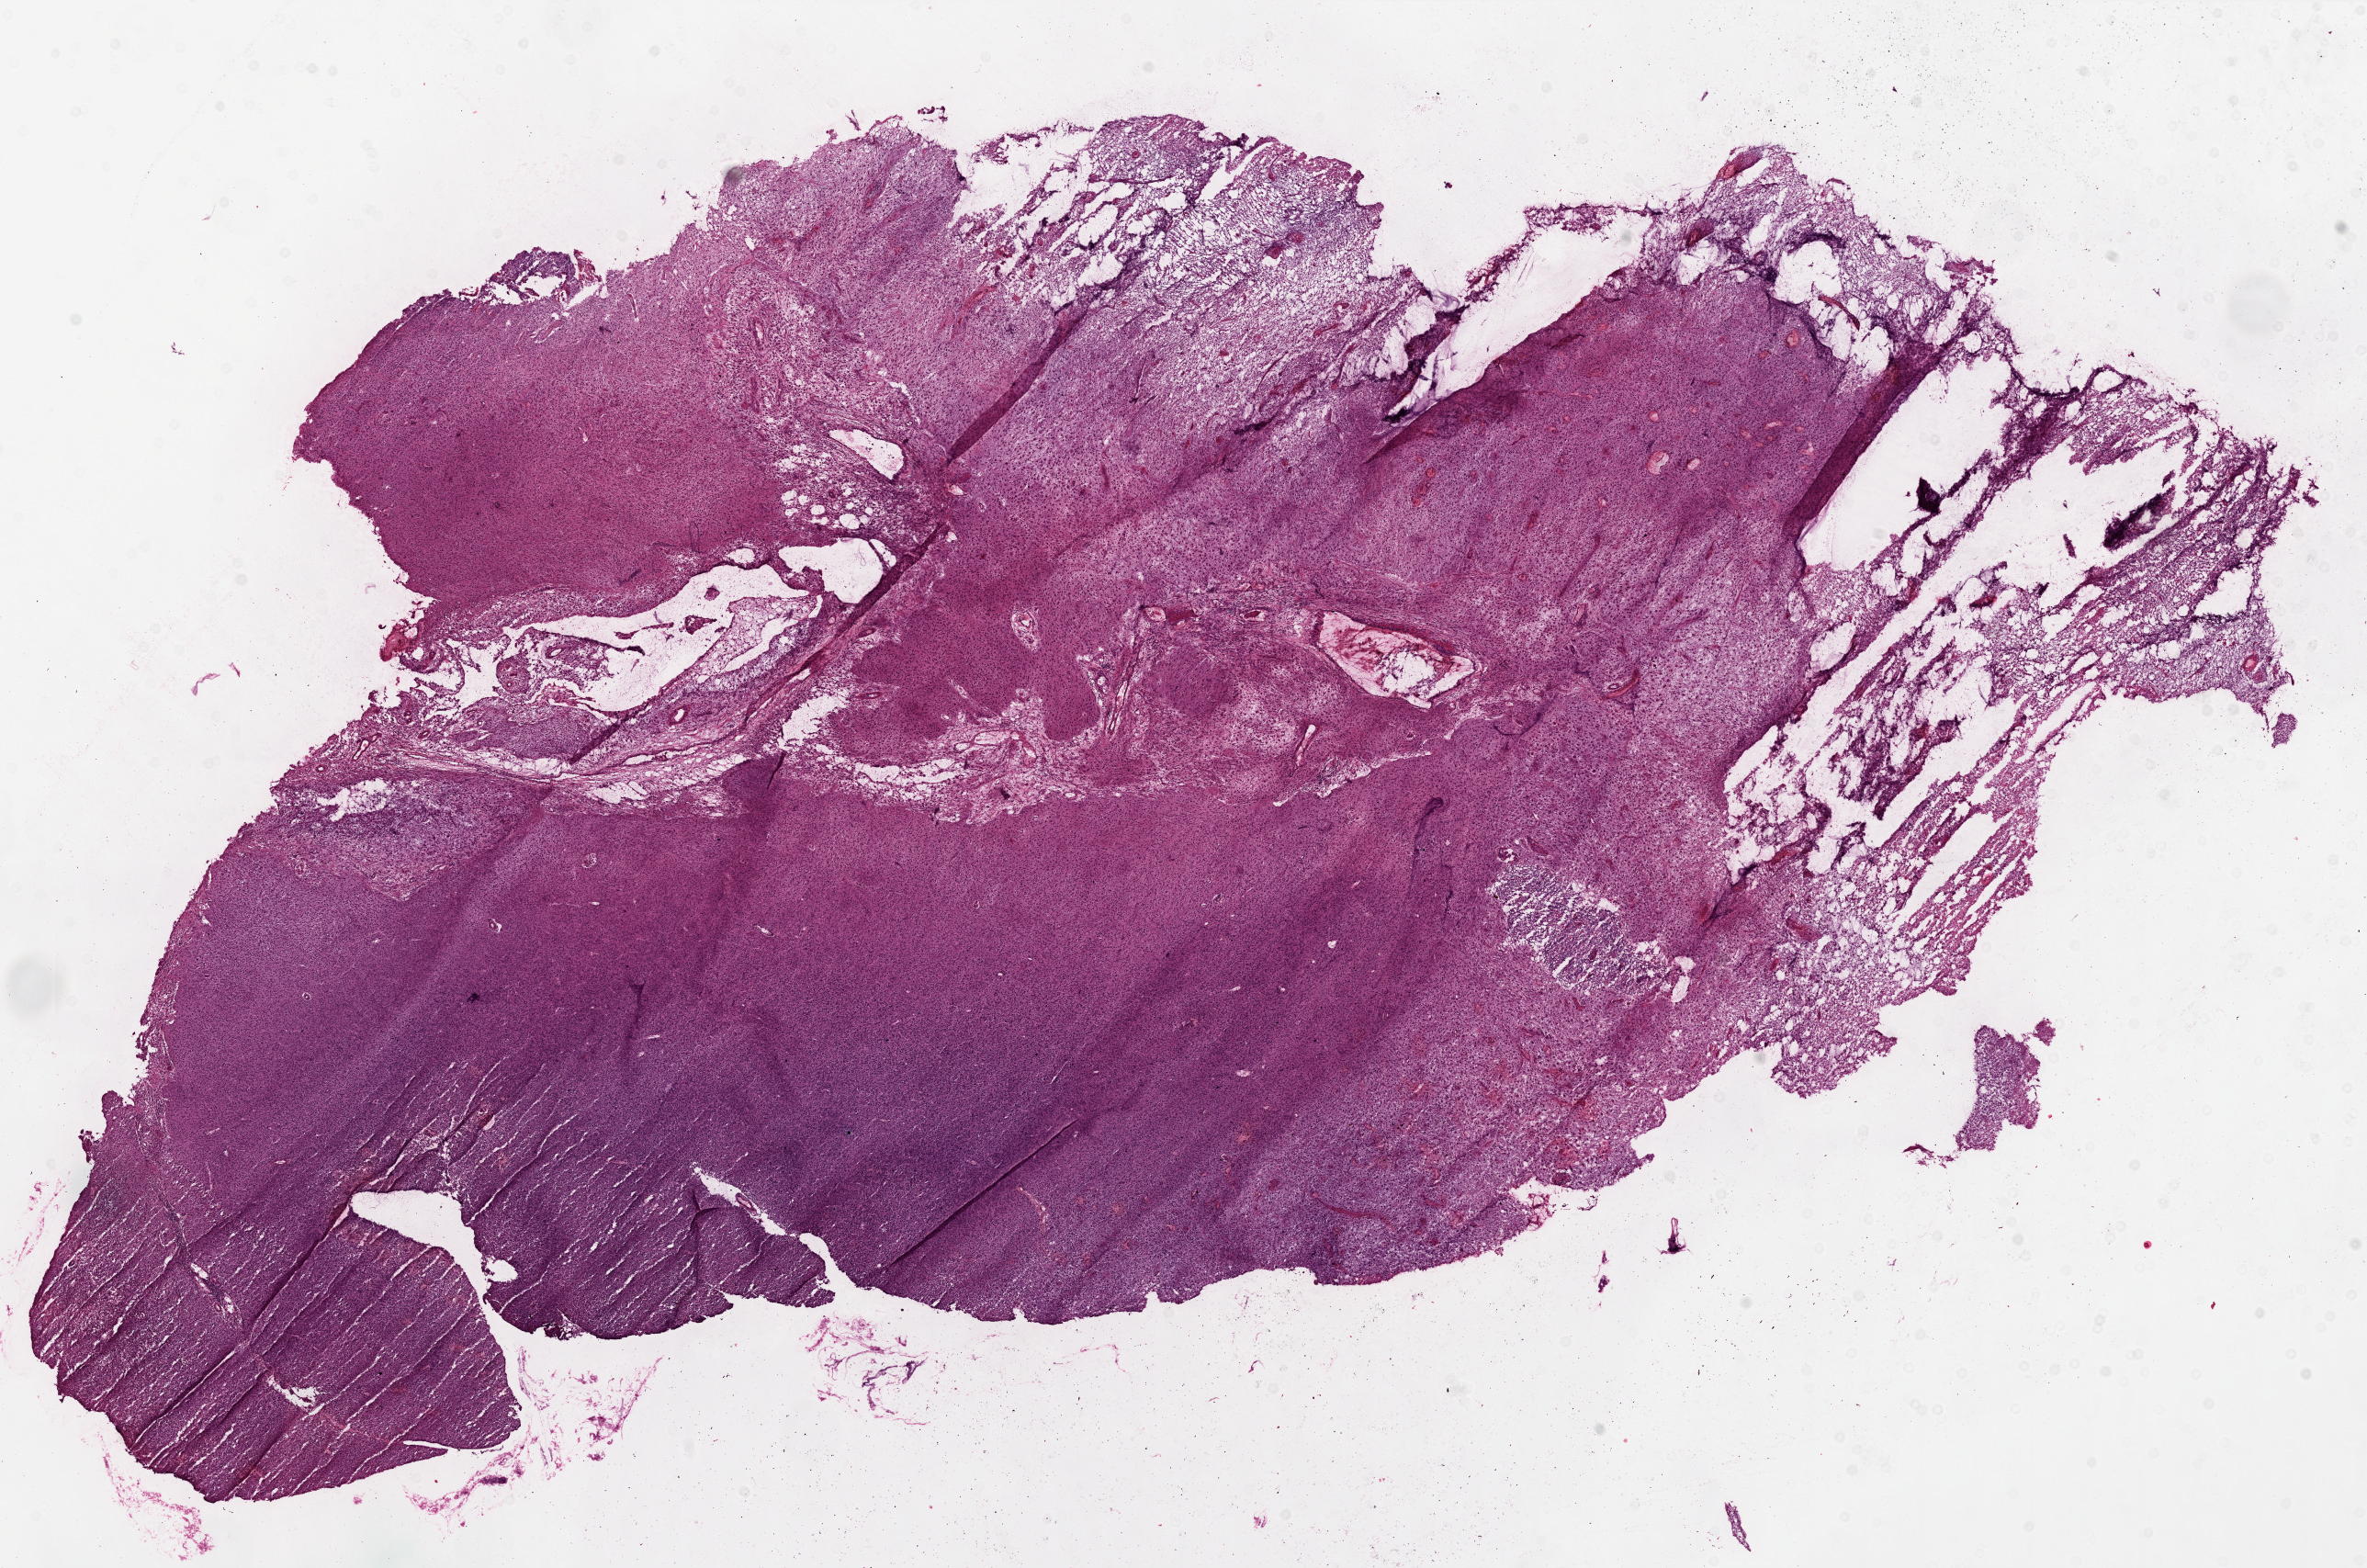
Whole-slide histology image, H&E — whole scanned area (about 20.7 x 13.7 mm) shown as a low-resolution overview. Frozen section. Brain, primary tumour sample. Male, age 57 years at initial diagnosis. Pathologist review of this section (percent, as recorded): tumour cells 80%, tumour nuclei 100%, normal cells 0%, stromal cells 0%, necrosis 20%.
* diagnosis: Glioblastoma